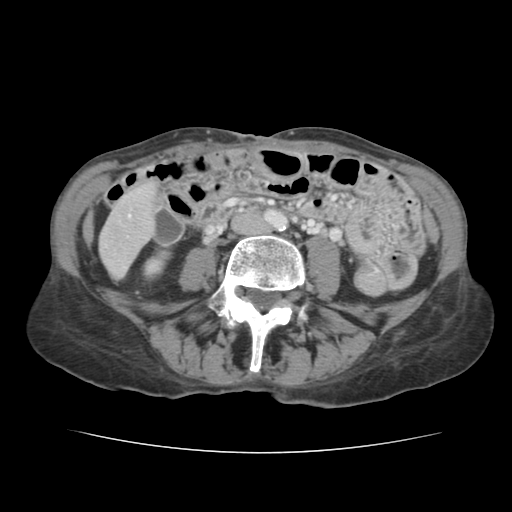
Contrast-enhanced abdominal CT, one axial slice; slice 21 of 136 in the series (ordered by position); 120 kVp; intravenous contrast given; soft-tissue window (W 400 / L 40 HU); 2.5 mm slice thickness; 512 × 512 image matrix, field of view 319 × 319 mm. Female patient, age 77 years. Case-level facts recorded for this patient, not image findings: diagnosis: colorectal cancer liver metastases, imaged before liver resection; multiple liver metastases: yes; largest metastasis: 3 cm; chemotherapy before resection: yes.
Outlined on this slice (manually delineated by an expert):
- liver: box from (x=101, y=187) to (x=155, y=277) px